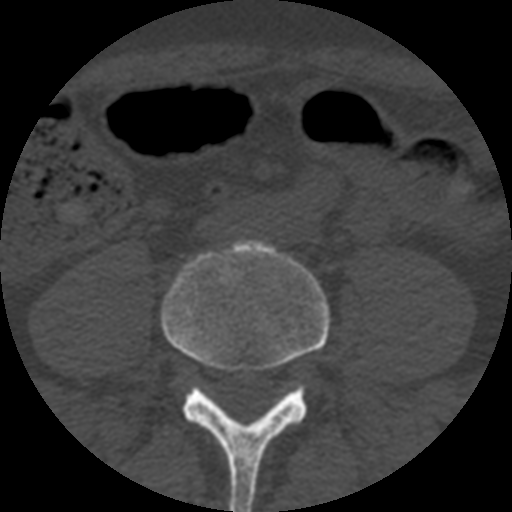
CT including the spine, one axial slice. Position 86 of 508 along the scan axis. Bone window (W 1800 / L 400 HU). 512 × 512 image matrix. Patient age 57 years. Case-level facts recorded for this patient, not image findings: primary cancer: prostate.
Annotated regions visible in this slice (semi-automatically segmented with operator editing):
- L4 vertebra: box from (x=161, y=241) to (x=329, y=512) px